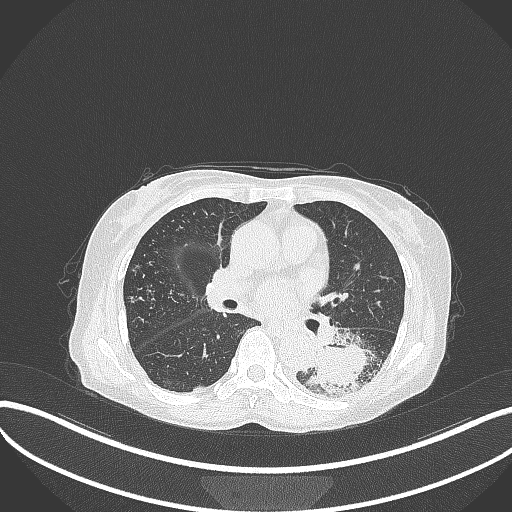
Chest CT, one axial slice; position 167 of 370 along the scan axis; lung window (W 1500 / L -600 HU); 1 mm slice thickness; 512 × 512 image matrix, field of view 400 × 400 mm. Patient: female, 78 years. Case-level facts recorded for this patient, not image findings: clinical TNM (as recorded): T3 N0 M1.
Structures marked on this image (bounding box drawn by a radiologist):
- lung tumour (recorded histology: squamous cell carcinoma): bounding box (x1, y1, x2, y2) in pixels: (309, 332, 384, 393)